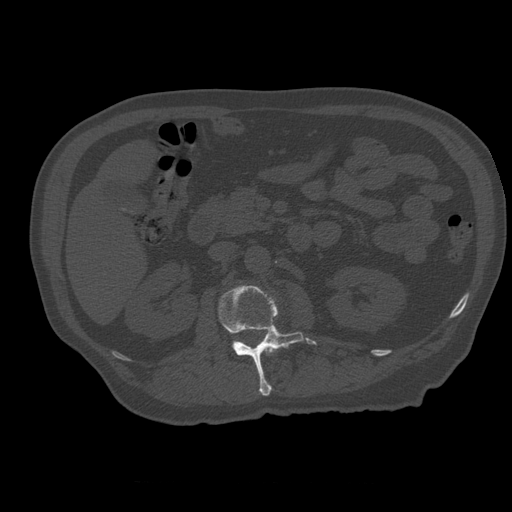
CT including the spine, one axial slice. Position 214 of 399 along the scan axis. 120 kVp. Bone window (W 1800 / L 400 HU). 512 × 512 image matrix, field of view 407 × 407 mm. Patient age 73 years. From the clinical record (not read from this slice): primary cancer: prostate; vertebrae with lytic lesions (as recorded): L2.
Structures marked on this image (semi-automatically segmented with operator editing):
- L1 vertebra: box from (x=265, y=347) to (x=279, y=355) px
- L2 vertebra: (x=217, y=286)–(x=304, y=396)